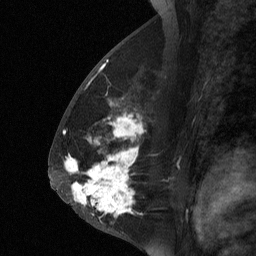
Breast MRI (dynamic contrast-enhanced), one sagittal slice; position 35 of 64 along the scan axis; dynamic contrast-enhanced study with each time point stored as its own series, time point 2 of 3 at this slice position (early post-contrast, ordered by acquisition time); 1.5 T; TE 4.8 ms, TR 27 ms; 2 mm slice thickness; 256 × 256 image matrix. Female patient, age 56 years. Case-level facts recorded for this patient, not image findings: setting: breast cancer imaged before/during neoadjuvant chemotherapy; receptor status: HER2-positive.
Structures marked on this image (semi-automatically segmented with operator editing):
- analysis volume of interest (the breast-tissue region the enhancement analysis was run in; not a lesion): bounding box (x1, y1, x2, y2) in pixels: (59, 104, 145, 229)
- tumour enhancement mask (voxels above the 90 % enhancement threshold inside the analysis volume of interest): (66, 161, 131, 213)